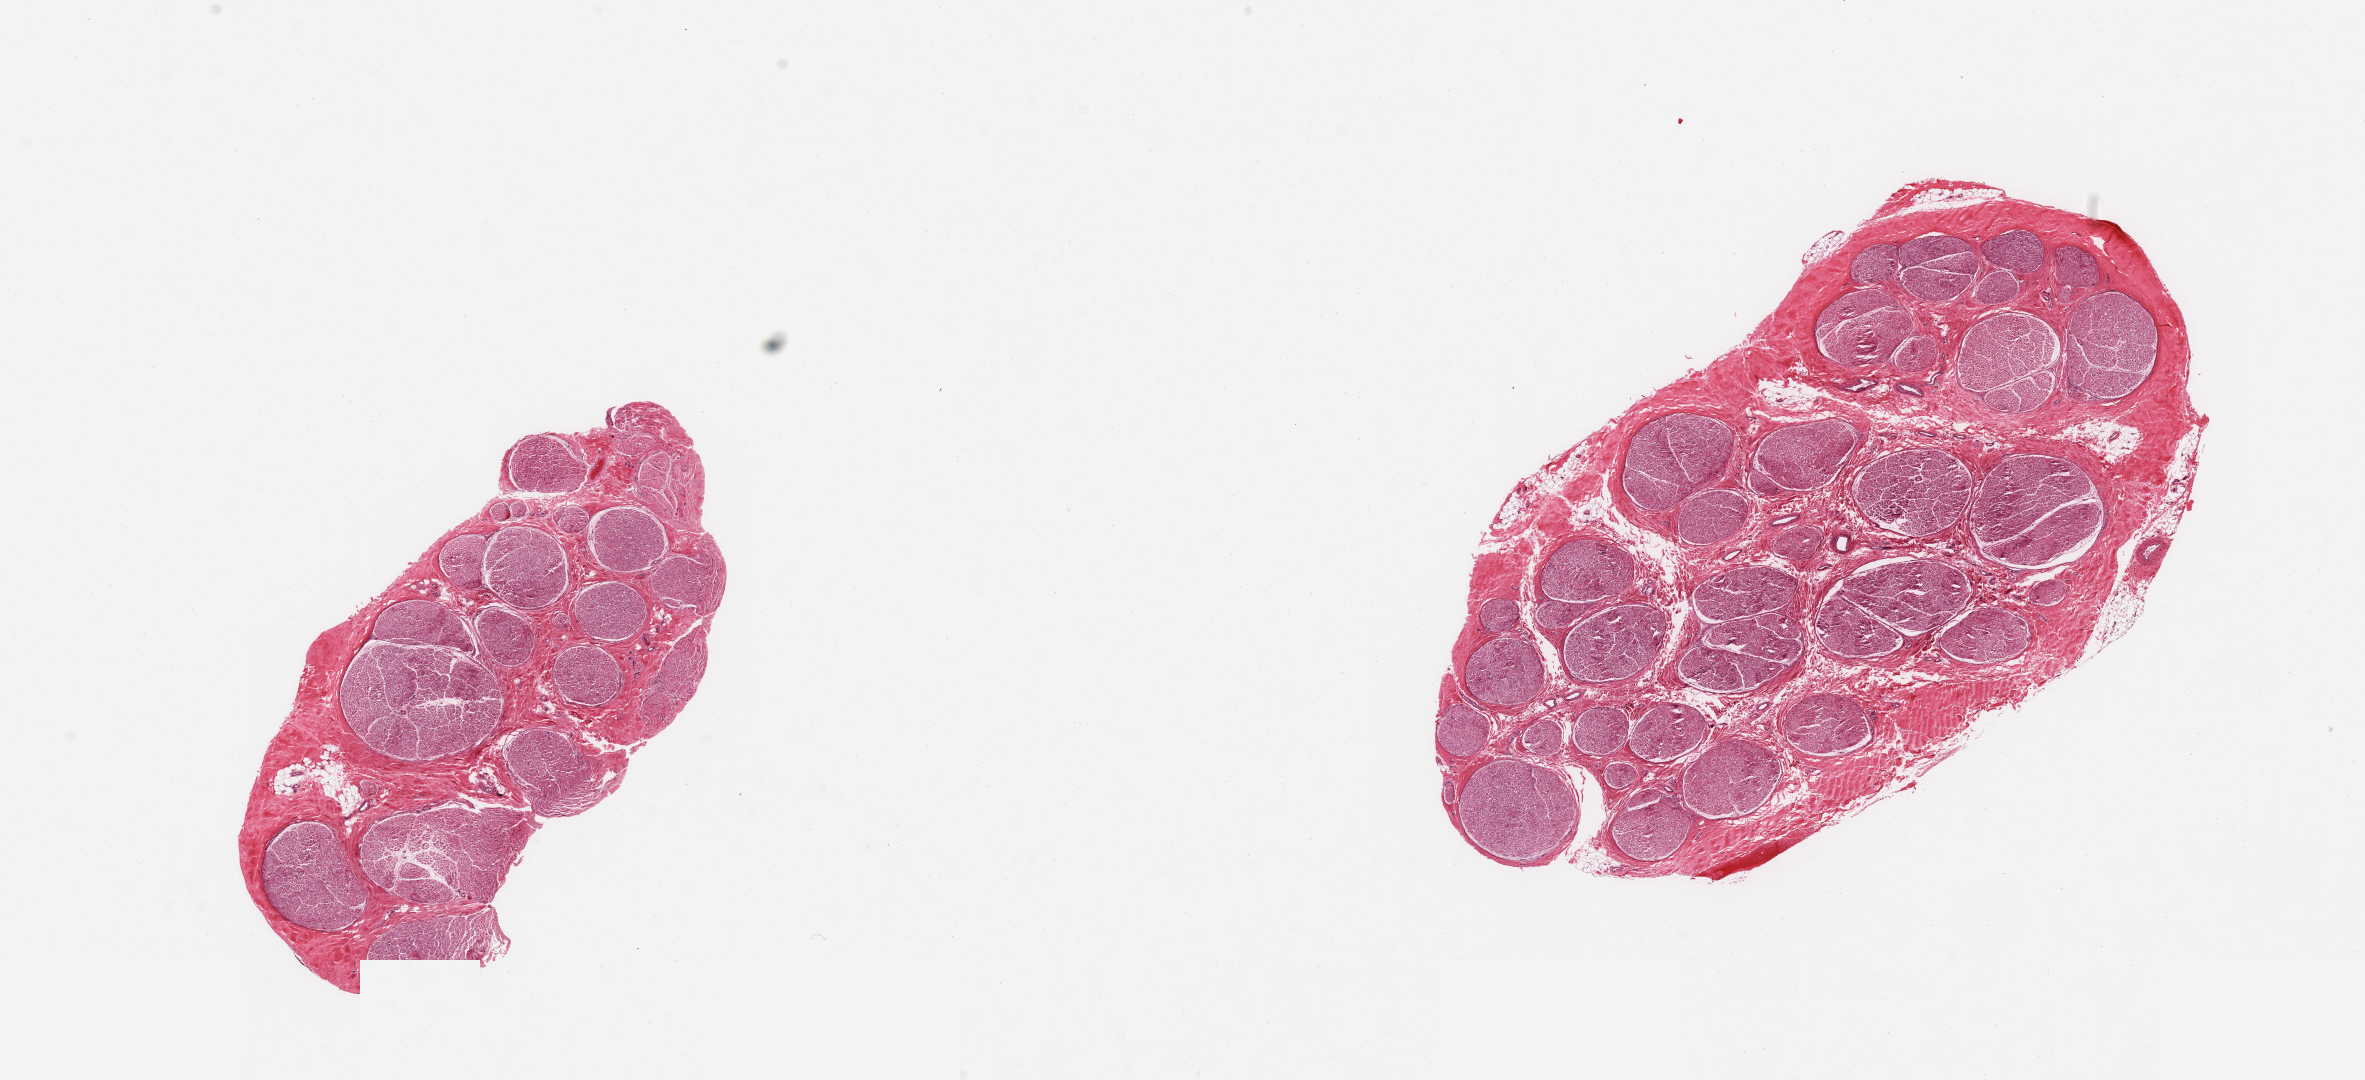
Hematoxylin and eosin (H&E) whole-slide image — shown as a low-resolution overview of the whole scanned area (about 18.7 x 8.5 mm), PAXgene-fixed paraffin-embedded (PFPE) section, sampled site (target tissue): tibial nerve, donor tissue sample. Donor: male.
Pathologist's review note for this sample: 2 pieces, no adherant fat.